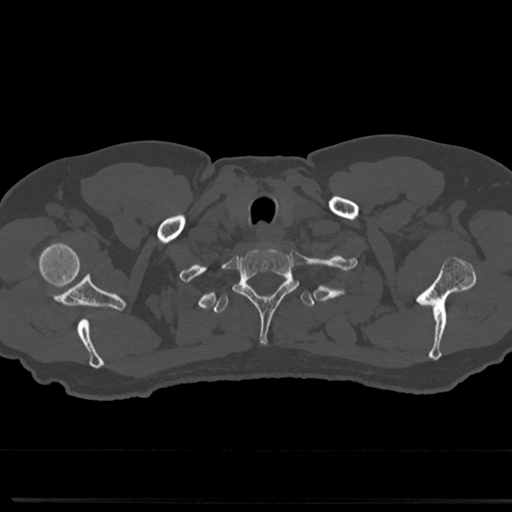
CT including the spine, one axial slice. Slice 666 of 817 in the series (ordered by position). Reconstruction kernel Br40s/3. Bone window (W 1800 / L 400 HU). 0.5 mm slice thickness. 512 × 512 image matrix. Patient: male, 61 years. From the clinical record (not read from this slice): primary cancer: prostate.
Outlined on this slice (semi-automatically segmented with operator editing):
- T1 vertebra: box from (x=234, y=247) to (x=297, y=341) px
- T2 vertebra: (x=212, y=277)–(x=315, y=315)